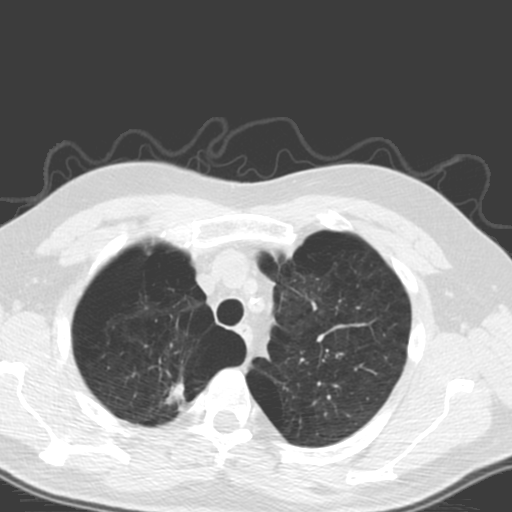
Low-dose screening chest CT, one axial slice; position 140 of 173 along the scan axis; 120 kVp; lung window (W 1500 / L -600 HU); 512 × 512 image matrix.
Outlined on this slice (expert manual segmentation):
- lesion 1 (tumor, upper lobe of right lung): bounding box [x1, y1, x2, y2] px = [165, 378, 185, 412]